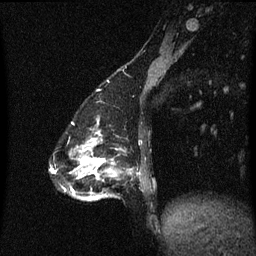
Breast MRI (dynamic contrast-enhanced), one sagittal slice; position 16 of 60 along the scan axis; dynamic contrast-enhanced series, image 2 of 3 at this slice position (ordered by acquisition); 1.5 T; TE 4.2 ms, TR 8.4 ms; 2 mm slice thickness; 256 × 256 image matrix. Female patient, age 47 years.
Annotated regions visible in this slice (semi-automatic segmentation, software-assisted and operator-edited):
- analysis volume of interest (the breast-tissue region the enhancement analysis was run in; not a lesion): box from (x=81, y=138) to (x=142, y=201) px
- tumour enhancement mask (voxels above the 70 % enhancement threshold inside the analysis volume of interest): (x=81, y=138)–(x=117, y=199)